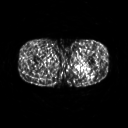
FDG PET of an extremity soft-tissue mass (from a PET/CT study), one axial slice. Position 239 of 267 along the scan axis. 3.27 mm slice thickness. 128 × 128 image matrix, field of view 500 × 500 mm. Male patient, age 27 years. From the clinical record (not read from this slice): histological type: extraskeletal osteosarcoma; grade: high; site of the primary tumour: left adductur.
Structures marked on this image (expert contour drawn on MRI and transferred to this co-registered scan by the dataset authors):
- gross tumour volume (mass): bounding box [x1, y1, x2, y2] px = [70, 61, 95, 75]